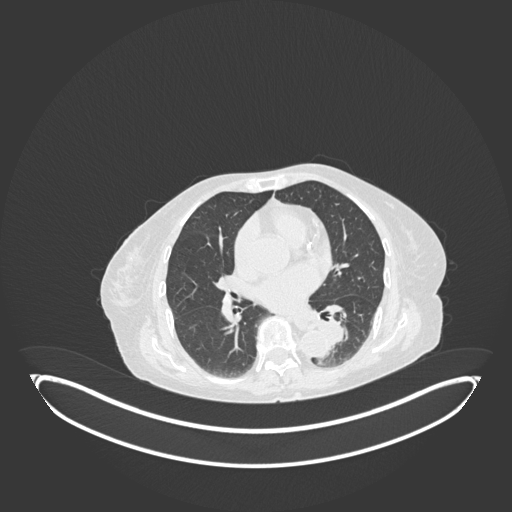
Chest CT, one axial slice. Reconstruction kernel B30f. 120 kVp. Lung window (W 1500 / L -600 HU). 1 mm slice thickness. 512 × 512 image matrix. Patient: female, 82 years. From the clinical record (not read from this slice): clinical TNM (as recorded): T1b N0 M1.
Structures marked on this image (rectangle marked by the reading radiologist):
- lung tumour (recorded histology: adenocarcinoma): bounding box (x1, y1, x2, y2) in pixels: (314, 314, 352, 352)